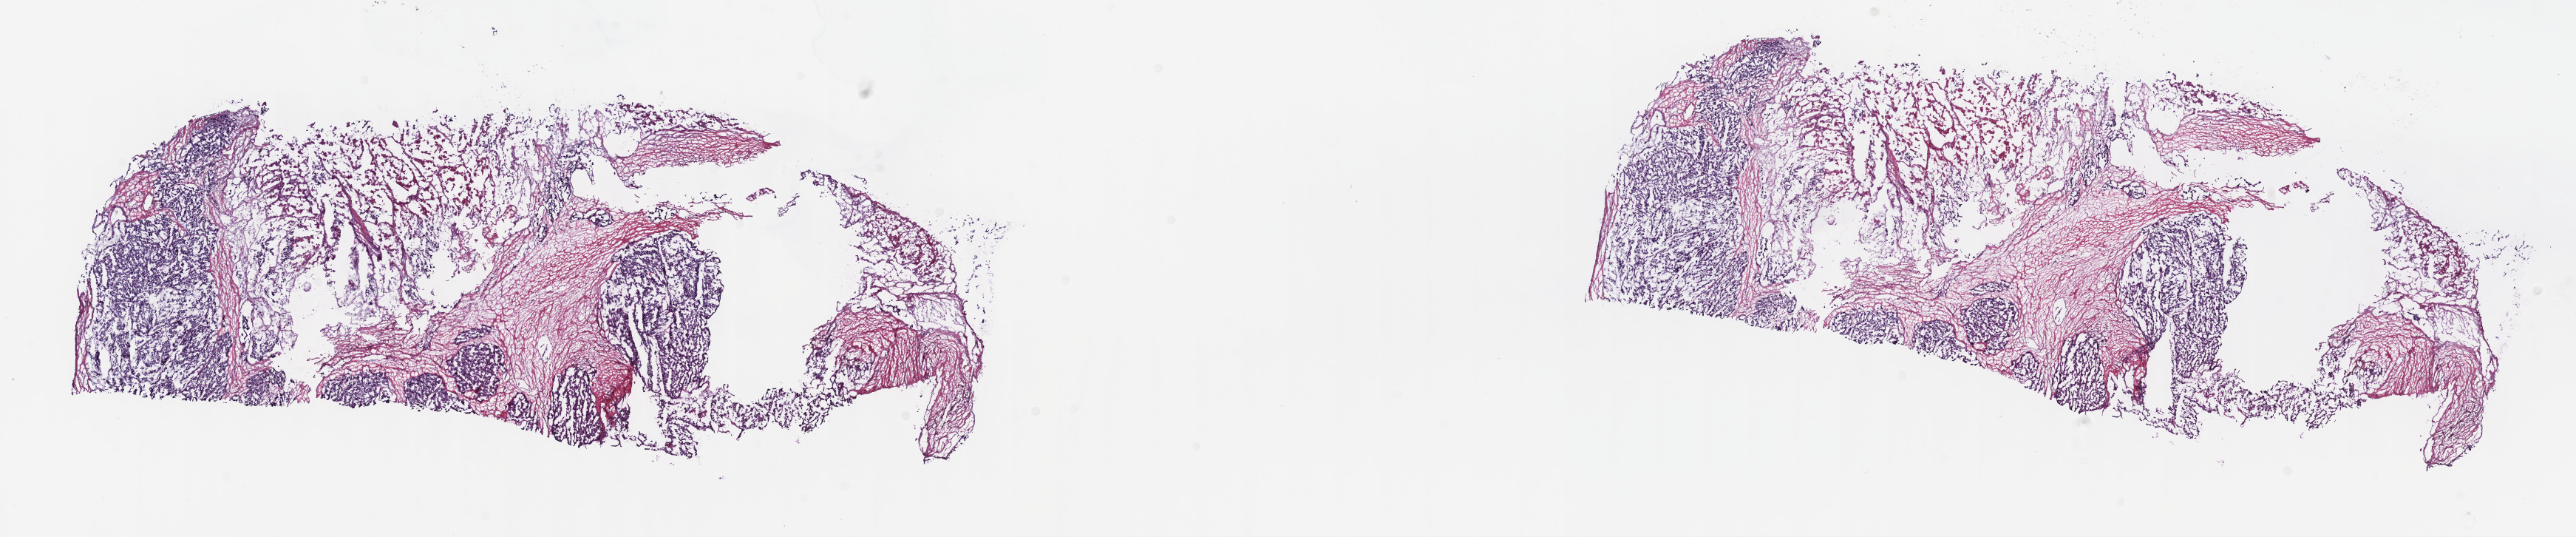
Hematoxylin and eosin (H&E) stained whole-slide image, whole scanned area (about 28.2 x 5.9 mm) shown as a low-resolution overview; formalin-fixed paraffin-embedded (FFPE) diagnostic section; primary tumour sample from the breast. Patient: female, age at initial diagnosis 35 years.
Pathologic diagnosis: Infiltrating duct carcinoma, NOS. AJCC pathologic stage: IV.